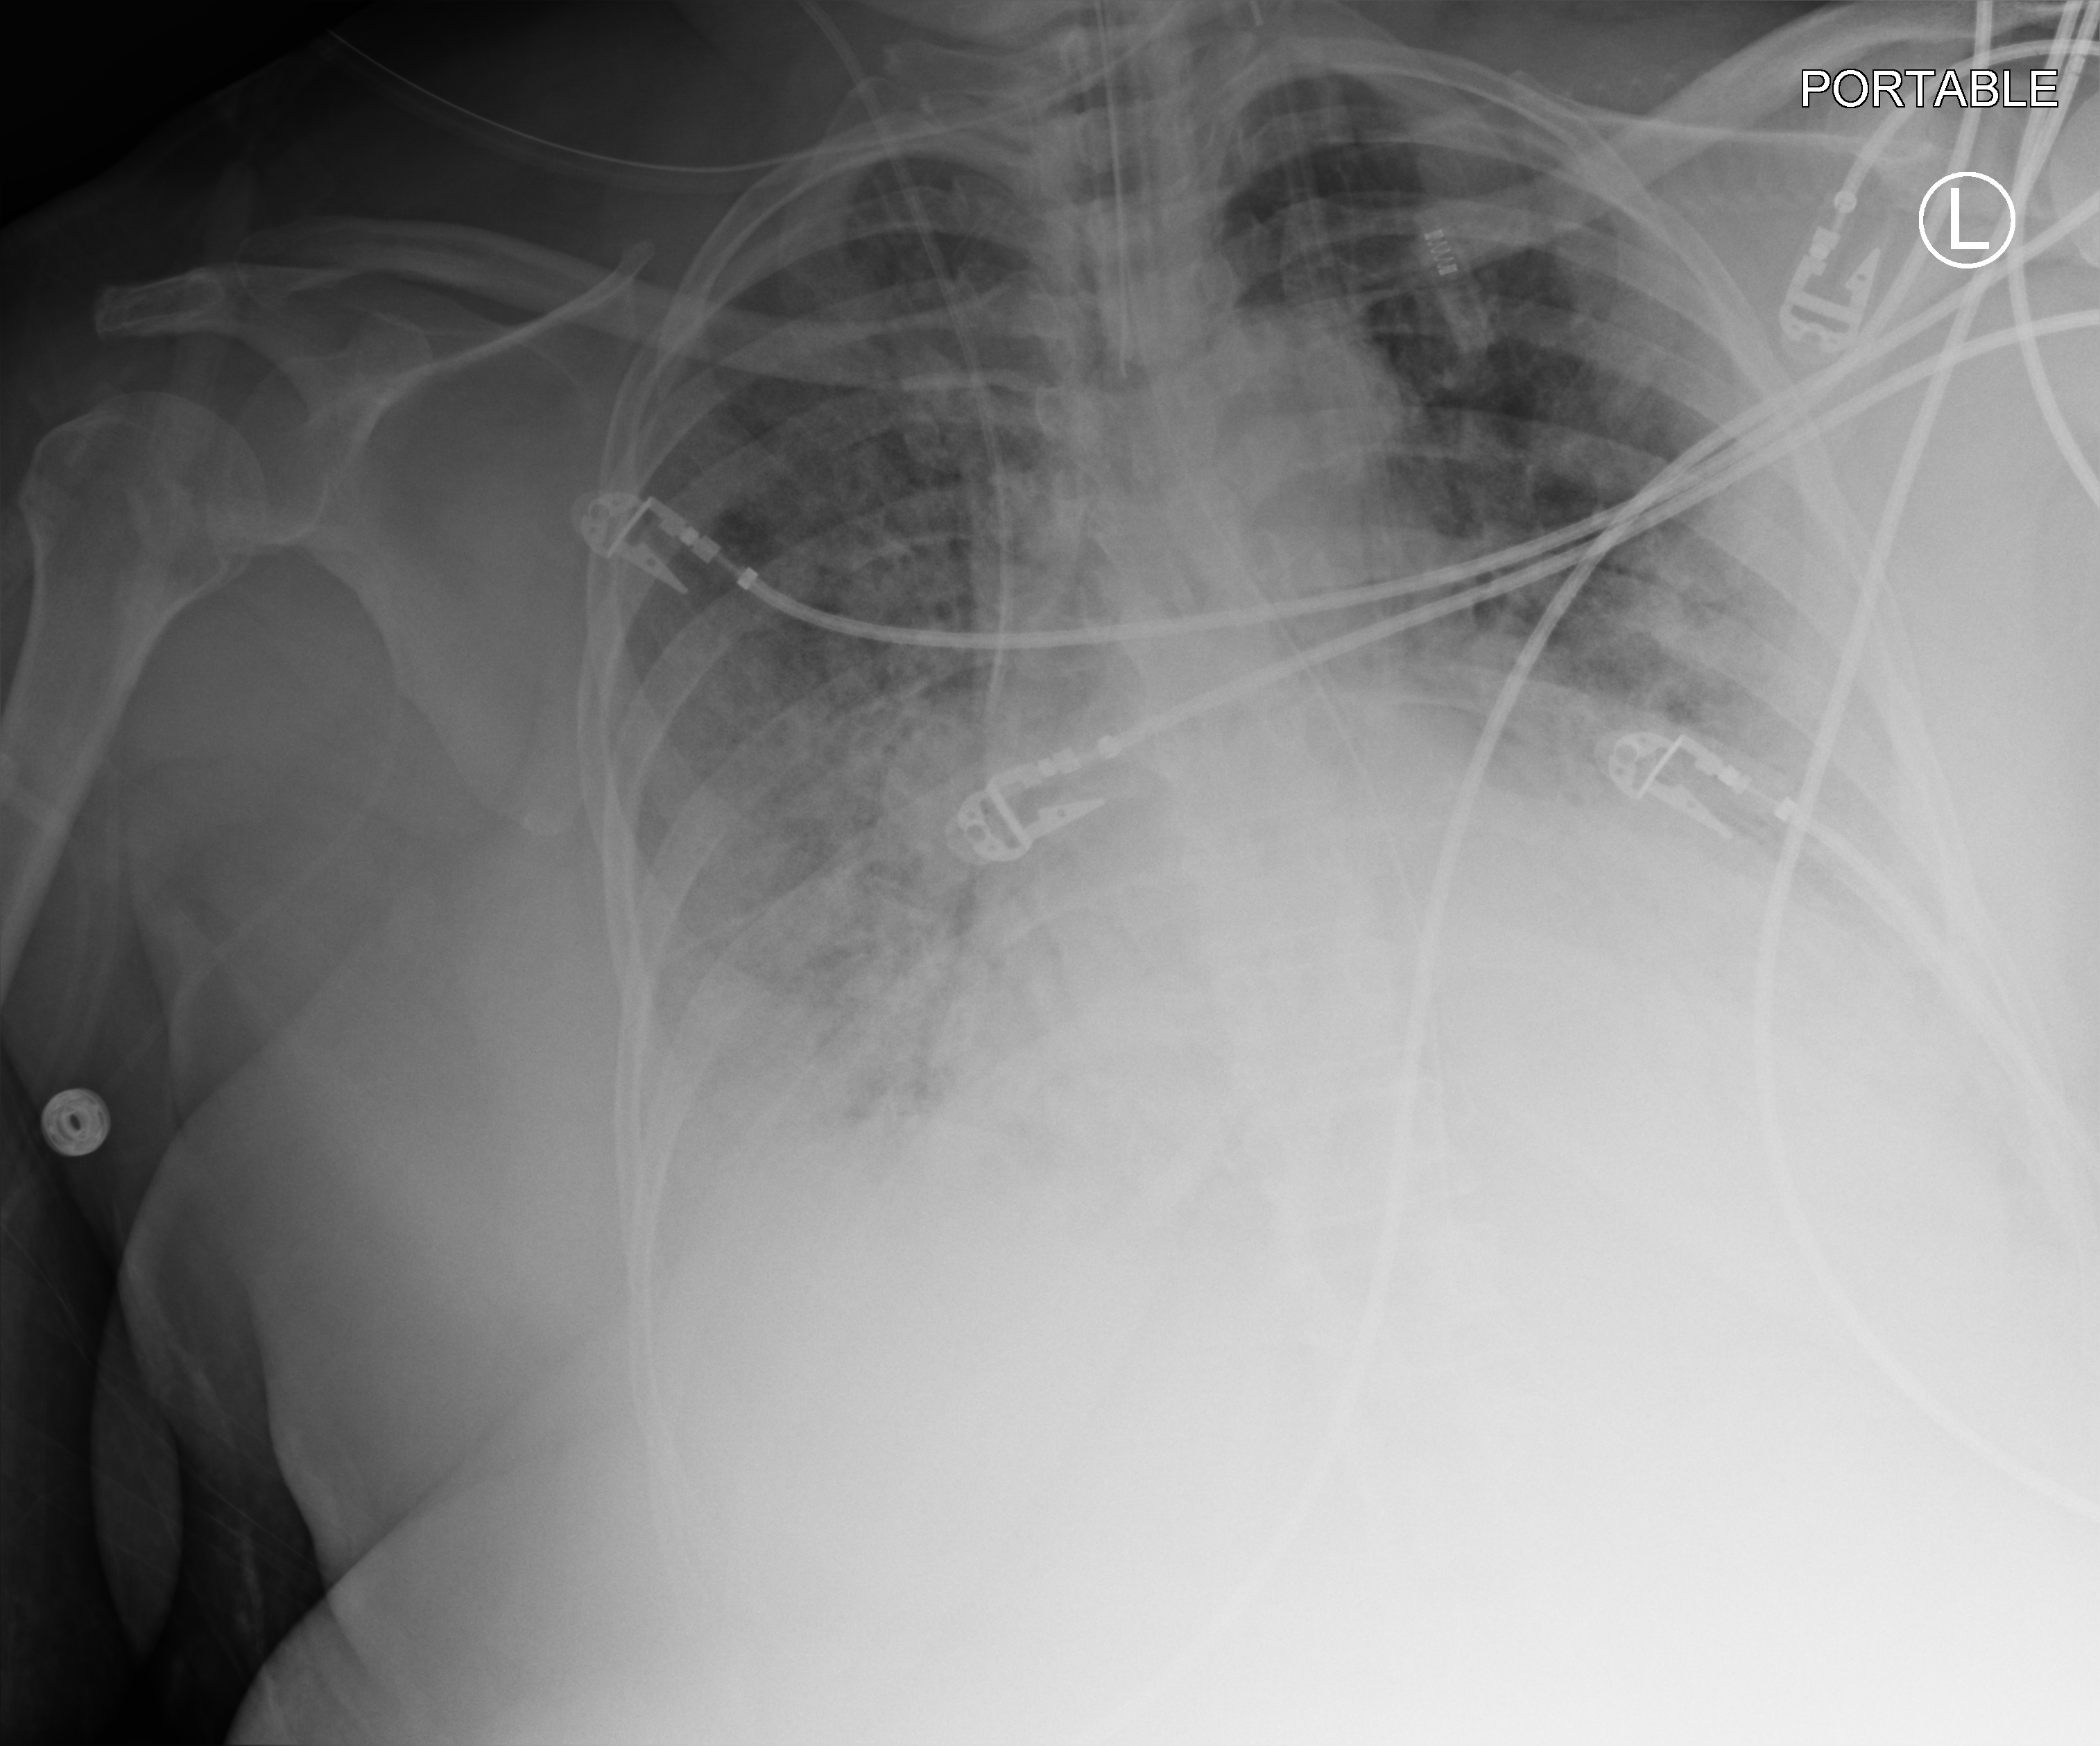
Bedside chest radiograph (computed radiography). Patient hospitalised with COVID-19; female, aged 60–74 years.
Hospital-stay facts (about this admission, not read from this image; timing relative to this image not recorded):
- admitted to intensive care during this hospital stay: yes